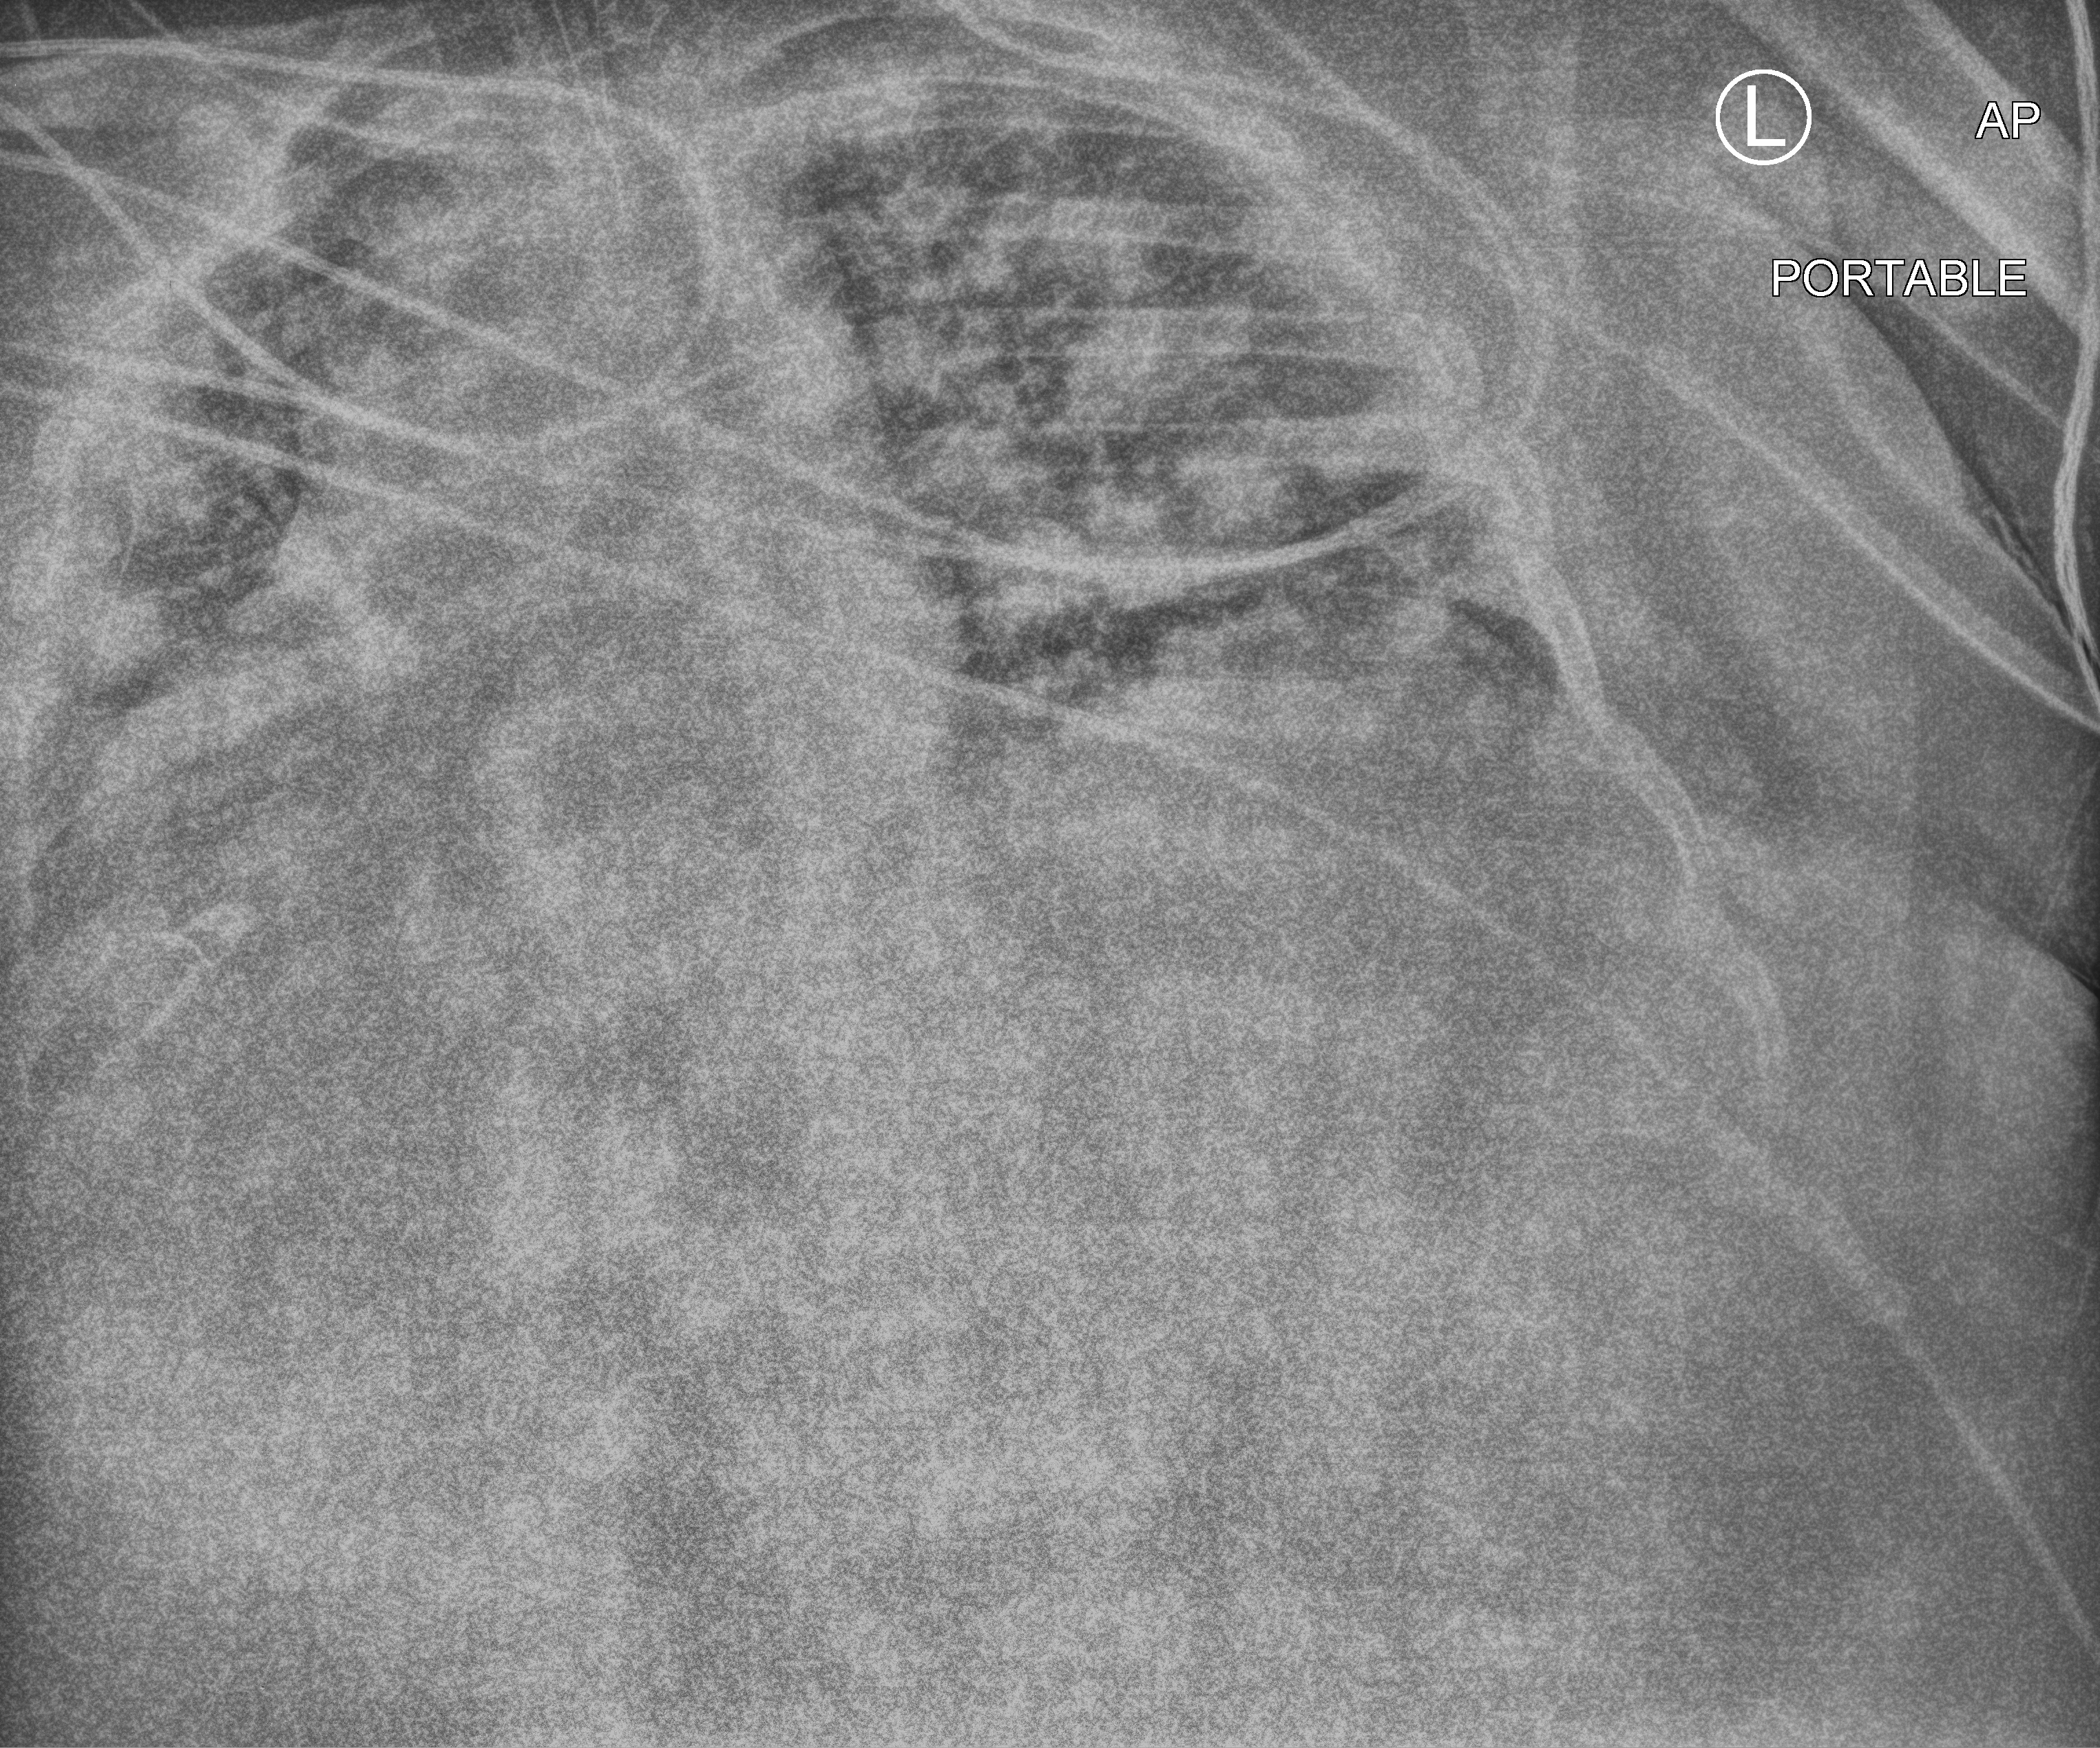
Bedside chest radiograph (computed radiography). Patient hospitalised with COVID-19; male, aged 18–59 years.
Hospital-stay facts (about this admission, not read from this image; timing relative to this image not recorded): admitted to intensive care during this hospital stay: yes; diabetes (admission record): yes.